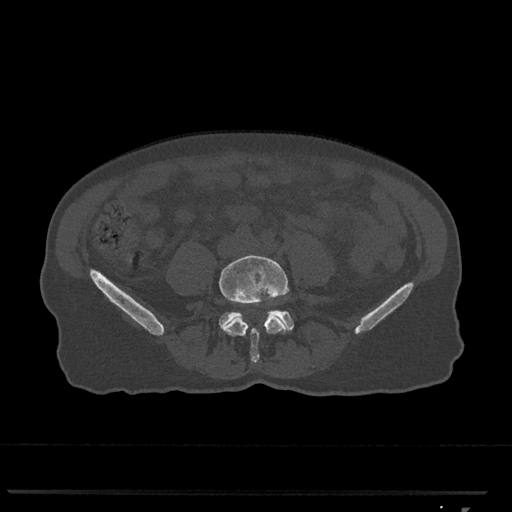
CT including the spine, one axial slice. Position 186 of 793 along the scan axis. Bone window (W 1800 / L 400 HU). 512 × 512 image matrix. Female patient, age 62 years. From the clinical record (not read from this slice): primary cancer: renal.
Structures marked on this image (semi-automatically segmented with operator editing):
- L4 vertebra: bounding box [x1, y1, x2, y2] px = [219, 255, 290, 363]
- L5 vertebra: [219, 310, 294, 331]